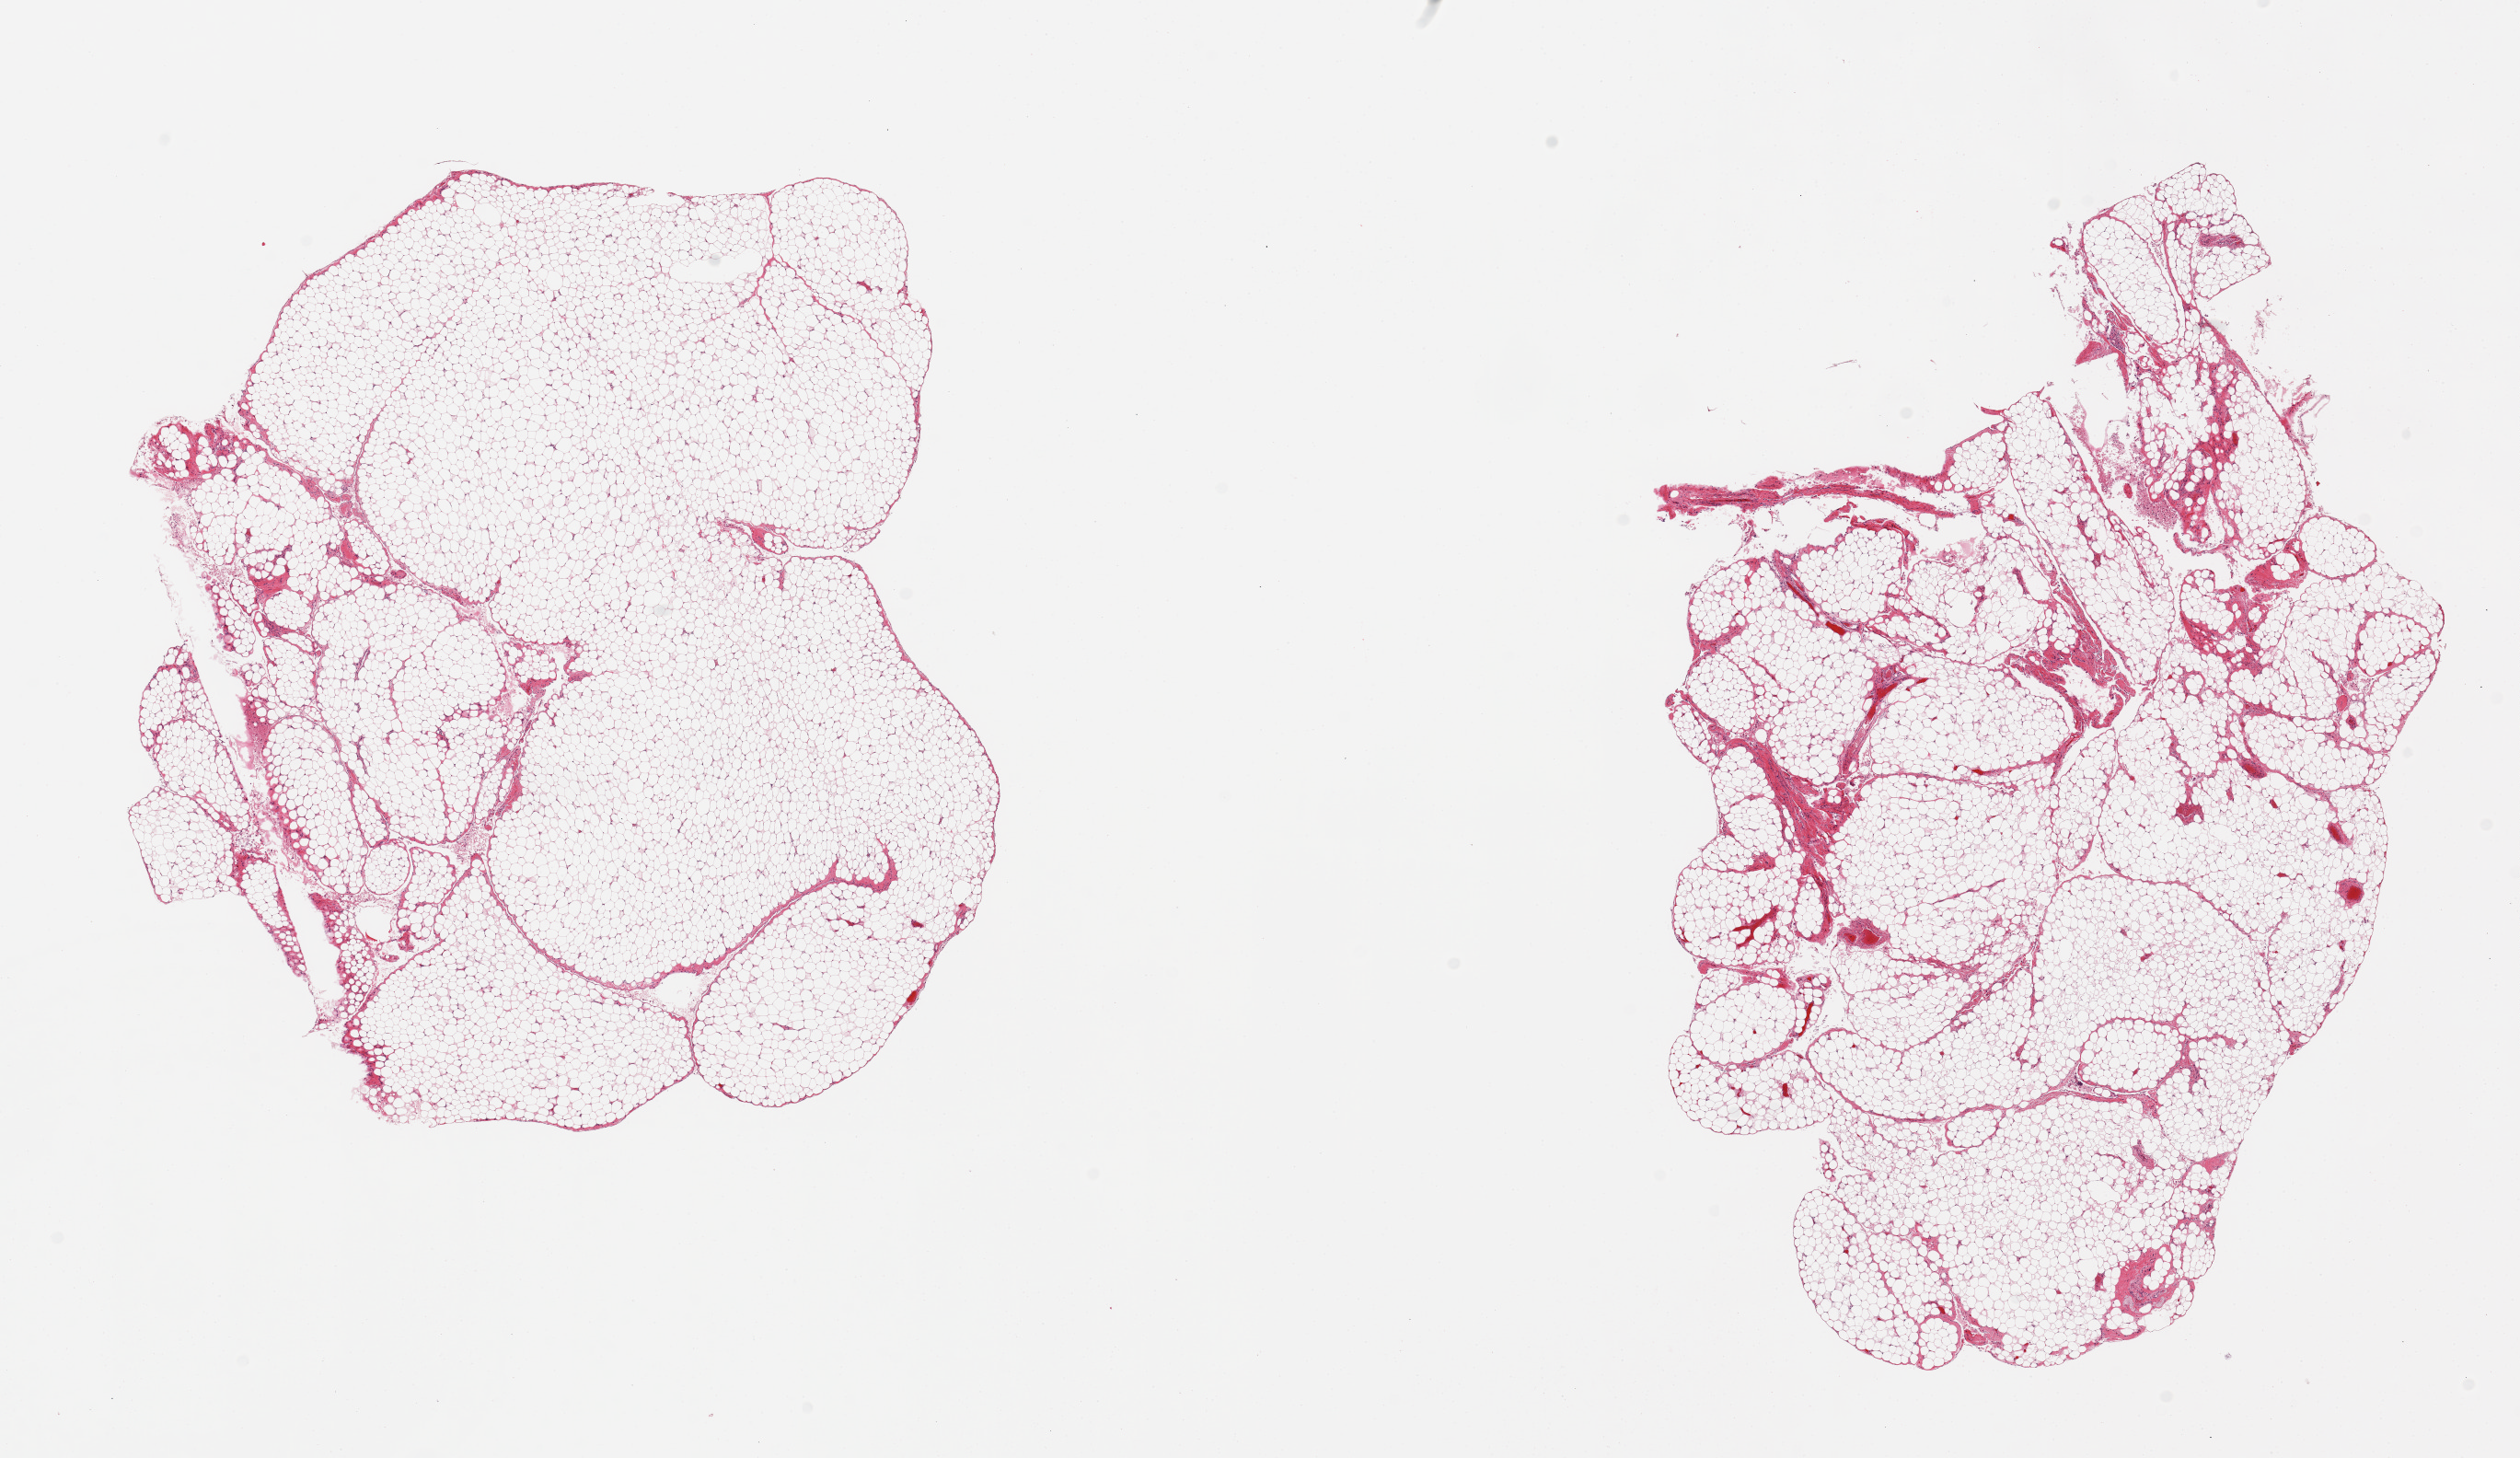
Hematoxylin and eosin (H&E) whole-slide image, brightfield, a low-resolution overview of the entire scanned area, about 21.7 x 12.5 mm (slide scanned at 20x), PAXgene-fixed, paraffin-embedded tissue, target tissue: omentum, tissue donor sample. Donor sex: male.
Review note (as recorded): 2 pieces, `10-15% fibro-fascial/vascular tissue.